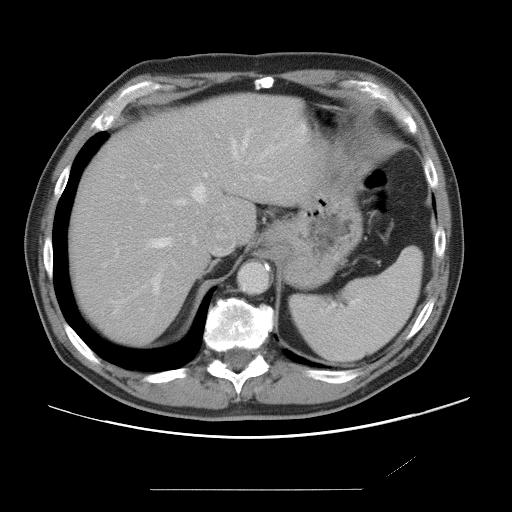
Contrast-enhanced abdominal CT, one axial slice. Position 57 of 87 along the scan axis. 120 kVp. Intravenous contrast given. Soft-tissue window (W 400 / L 40 HU). 512 × 512 image matrix, field of view 406 × 406 mm. Male patient, age 74 years. From the clinical record (not read from this slice): diagnosis: colorectal cancer liver metastases, imaged before liver resection; multiple liver metastases: yes; largest metastasis: 1.1 cm; disease in both lobes: no.
Structures marked on this image (expert manual segmentation):
- hepatic veins: bounding box [x1, y1, x2, y2] px = [152, 129, 268, 292]
- liver: [72, 94, 310, 346]
- planned liver remnant (the part of the liver to remain after resection): [71, 94, 309, 346]
- portal vein (with intrahepatic branches): [115, 165, 207, 256]